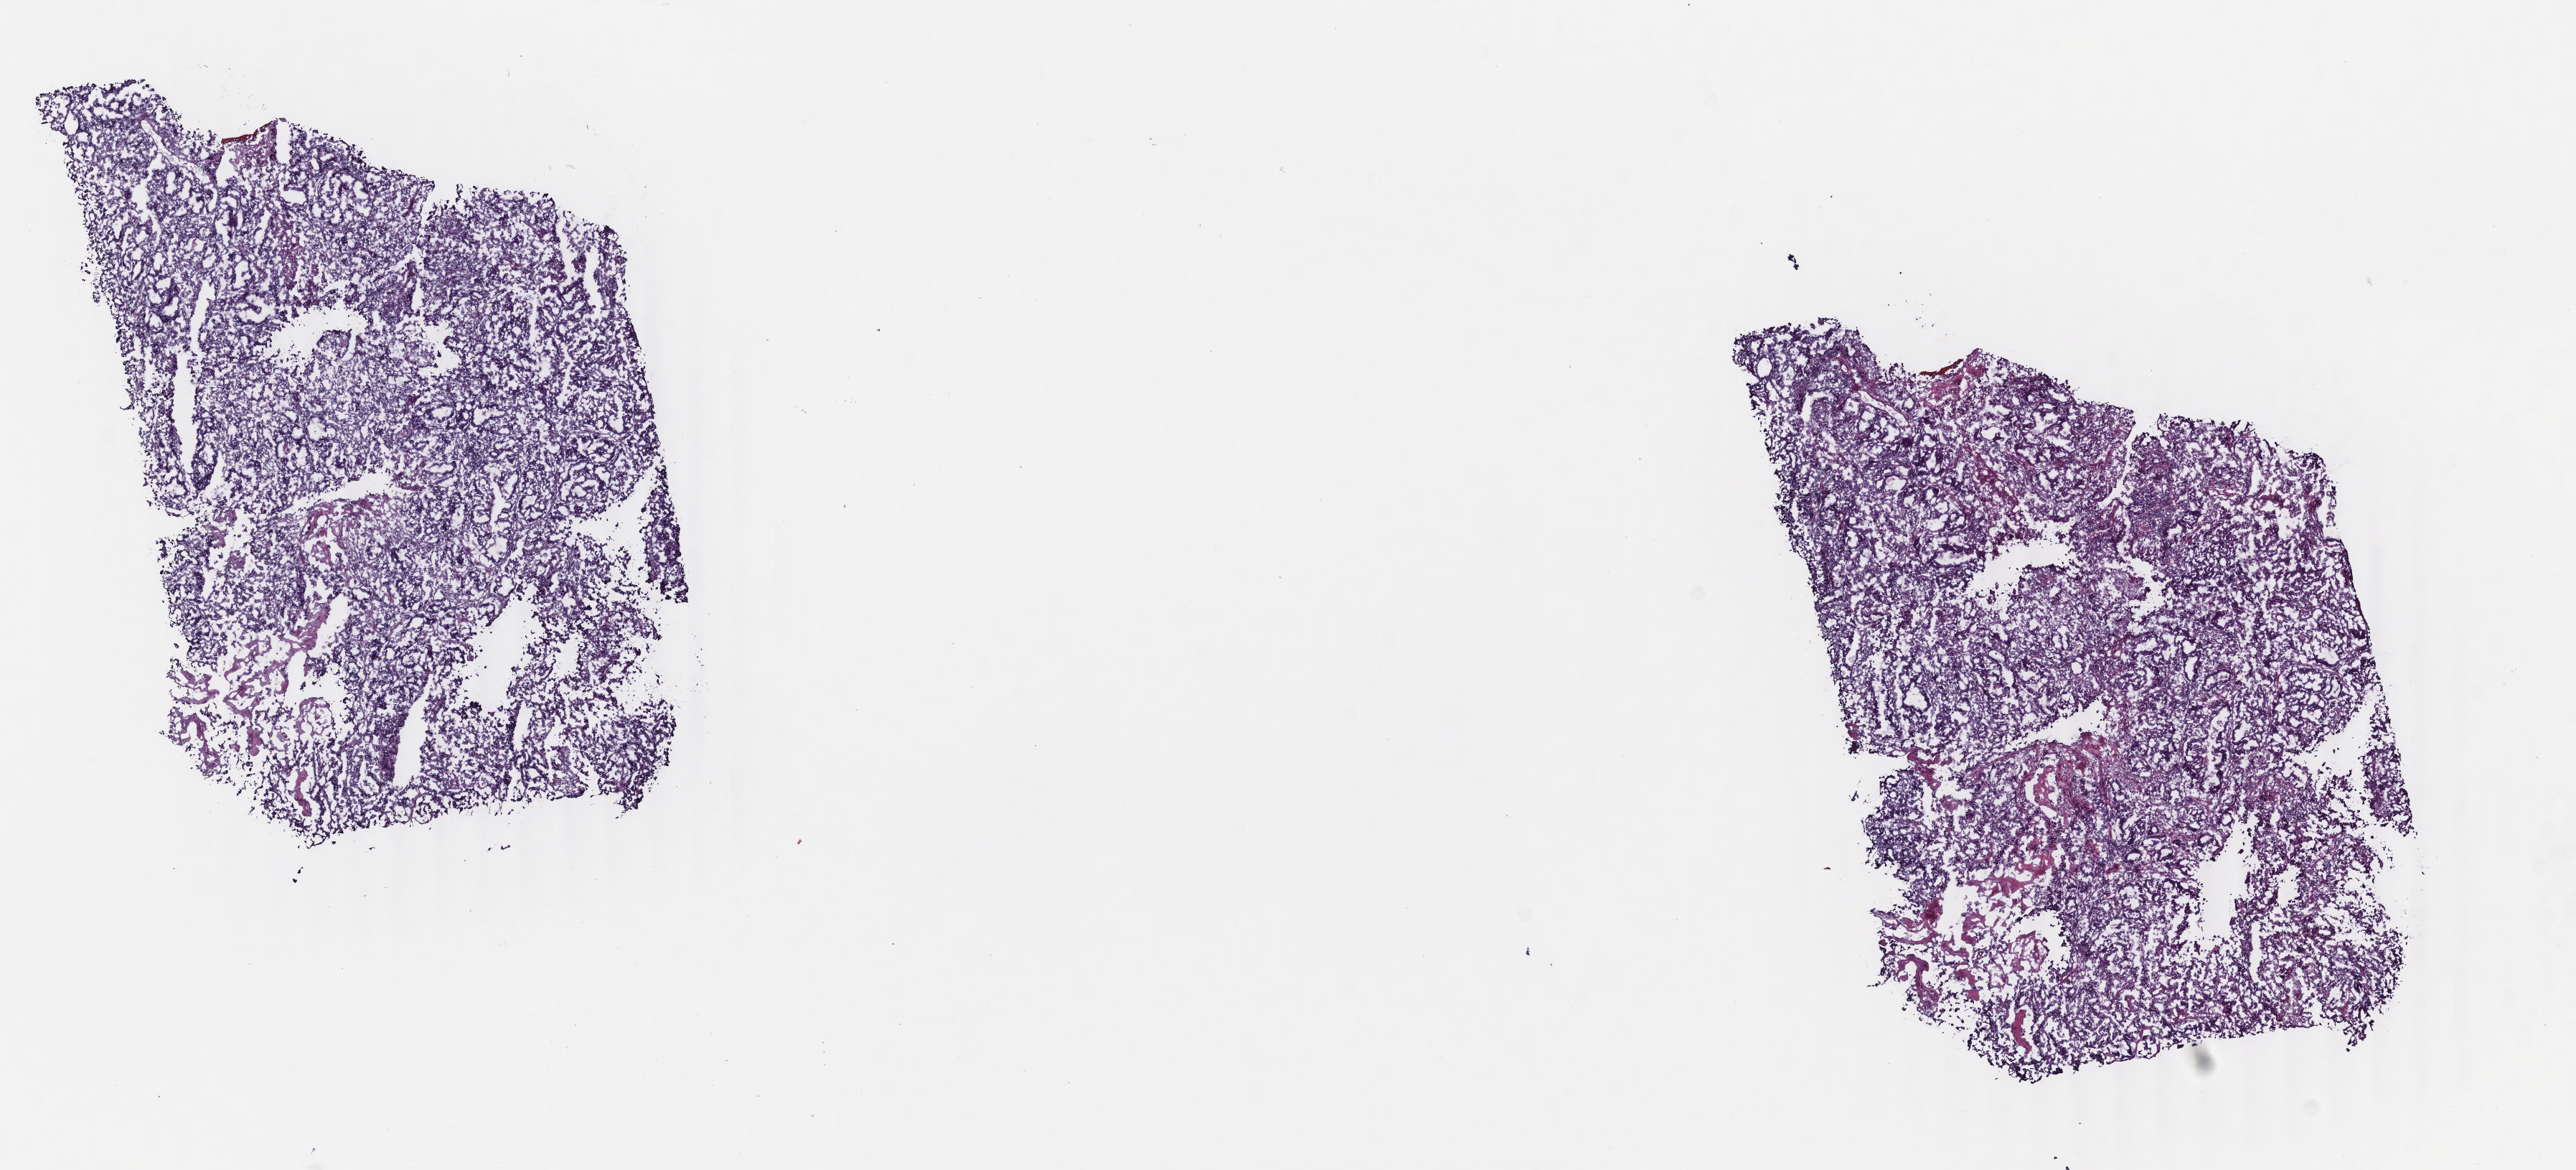
H&E whole-slide image — low-resolution overview of the scanned area, about 14.3 x 6.5 mm (from a 40x scan), frozen section from the top of the tissue portion, sample: primary tumour, uterus. Female, age 67 years at initial diagnosis. Histologic grade: G2 (moderately differentiated). Pathologist review of this section (percent, as recorded): tumour cells 85%, tumour nuclei 85%, normal cells 0%, stromal cells 5%, necrosis 10%. Inflammatory infiltration, as recorded: lymphocyte infiltration 5%, monocyte infiltration 10%, neutrophil infiltration 2%.
Histologic diagnosis: Endometrioid adenocarcinoma, NOS (endometrium). FIGO stage: IIIA.